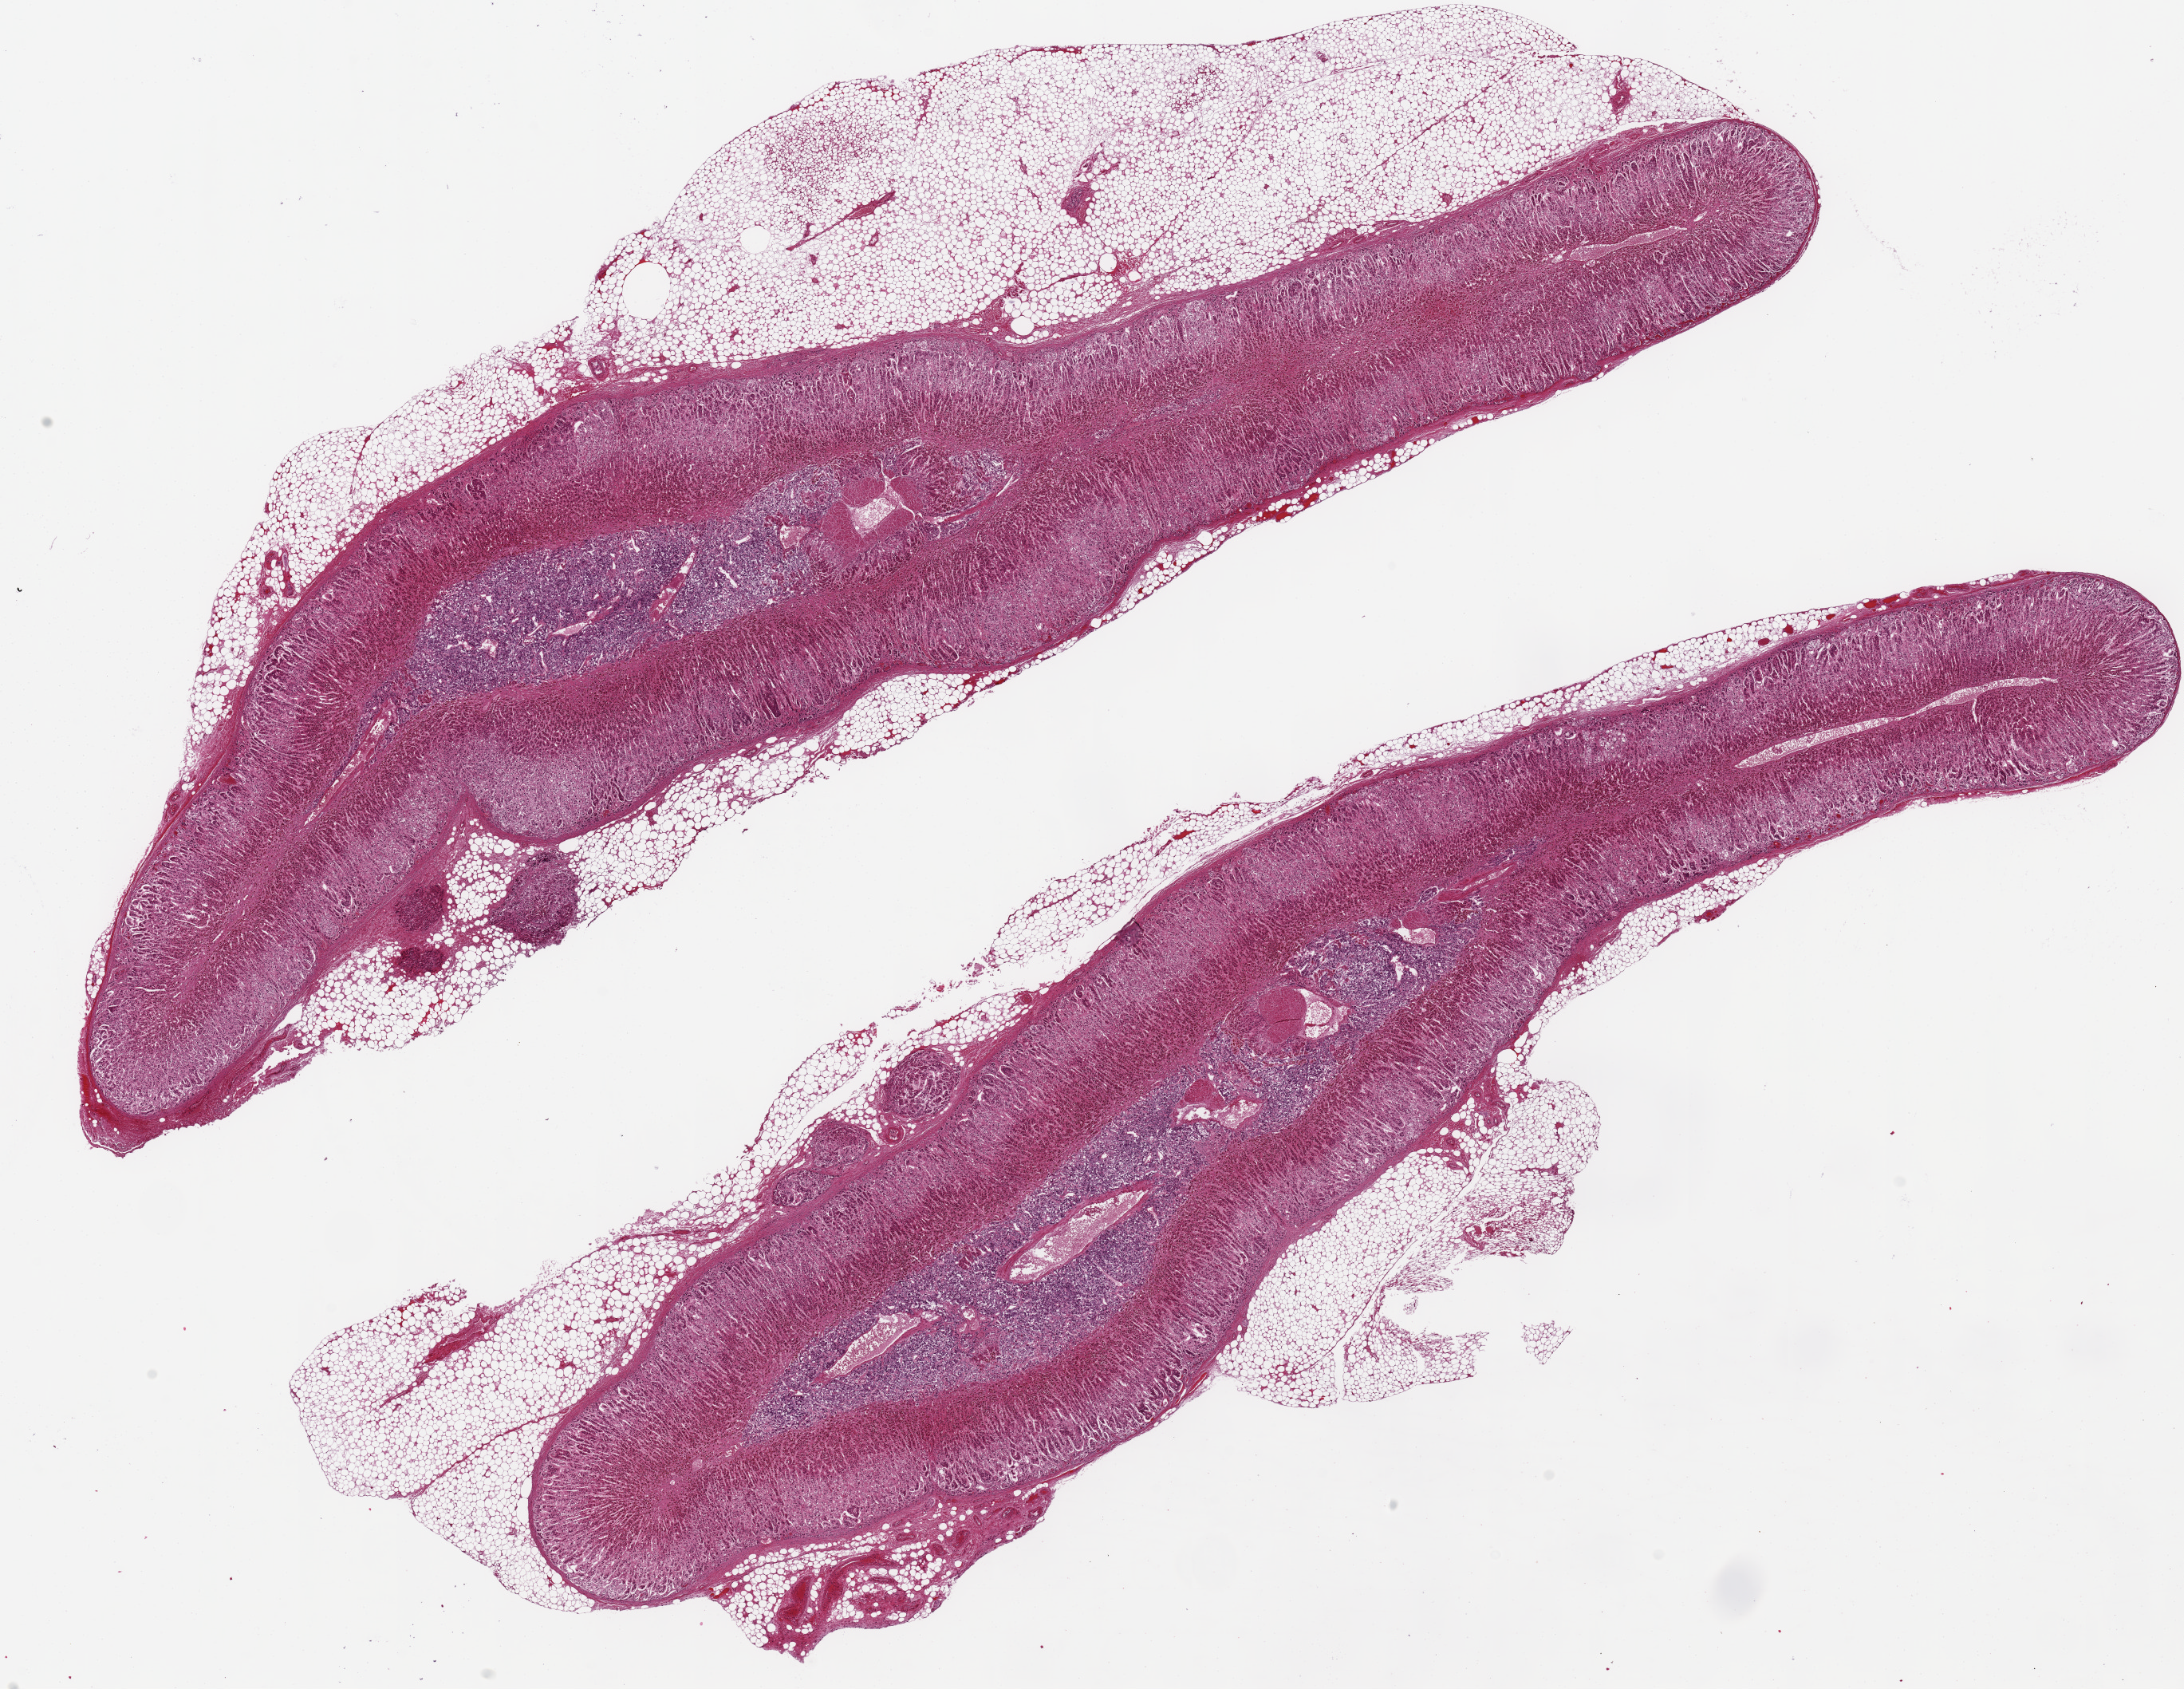
Digitized haematoxylin and eosin-stained section — whole scanned area (about 21.7 x 16.7 mm) shown as a low-resolution overview. PAXgene-fixed paraffin-embedded (PFPE) section. Target tissue: adrenal gland. Donor tissue sample.
Reviewer comment on this tissue sample: 2 ~18x3mm aliquots. Medulla well-visualized, ~15% of specimens, but badly autolyzed.